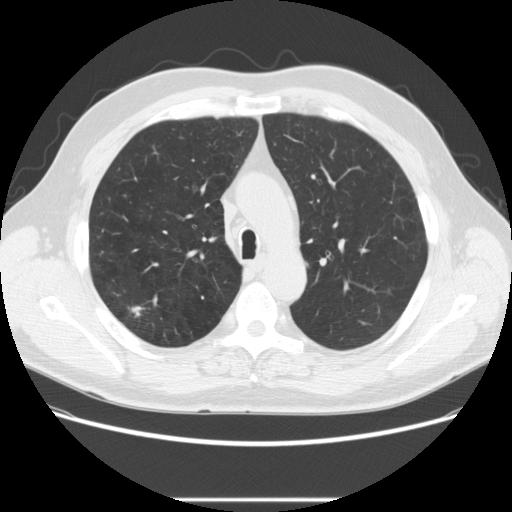
Chest CT (low-dose screening protocol), one axial image. First (baseline) screen. Lung window (W 1500 / L -600 HU). 2.5 mm slice thickness. Standard (soft-tissue) reconstruction kernel (STANDARD). 120 kVp. Slice 78 of 270 in the series. 512 × 512 image matrix. Male participant, aged 64 years at enrolment. Former smoker at enrolment.
Lesion marked by an expert reader, bounding box [x1, y1, x2, y2] px = [116, 298, 151, 326]. The screening reader recorded 2 non-calcified nodules or masses ≥4 mm on this exam; which of them this box marks is not recorded. Official screen result: positive, change unspecified: nodule(s) >= 4 mm or enlarging nodule(s), mass(es), or other non-specific abnormalities suspicious for lung cancer. Participant outcome: lung cancer diagnosed 753 days after this screen (after the third annual screen) — adenocarcinoma, NOS, right upper lobe, moderately differentiated (G2), stage IA (AJCC 6th edition), 14 mm at pathology.